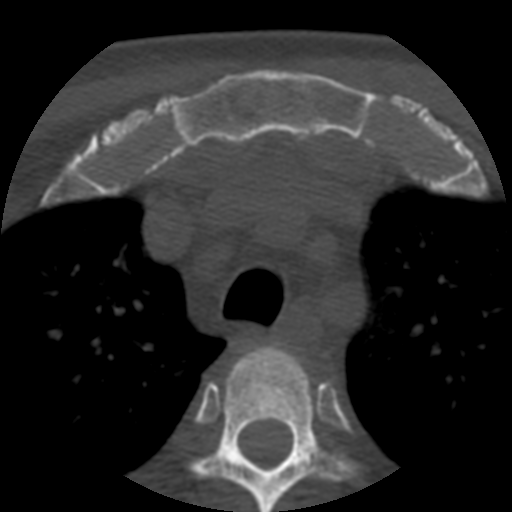
CT including the spine, one axial slice. Slice 415 of 508 in the series (ordered by position). Reconstruction kernel STANDARD. 120 kVp. Bone window (W 1800 / L 400 HU). 1.25 mm slice thickness. 512 × 512 image matrix, field of view 160 × 160 mm. Patient age 57 years. From the clinical record (not read from this slice): primary cancer: prostate.
Outlined on this slice (semi-automatically segmented with operator editing):
- T3 vertebra: bounding box [x1, y1, x2, y2] px = [194, 344, 352, 512]